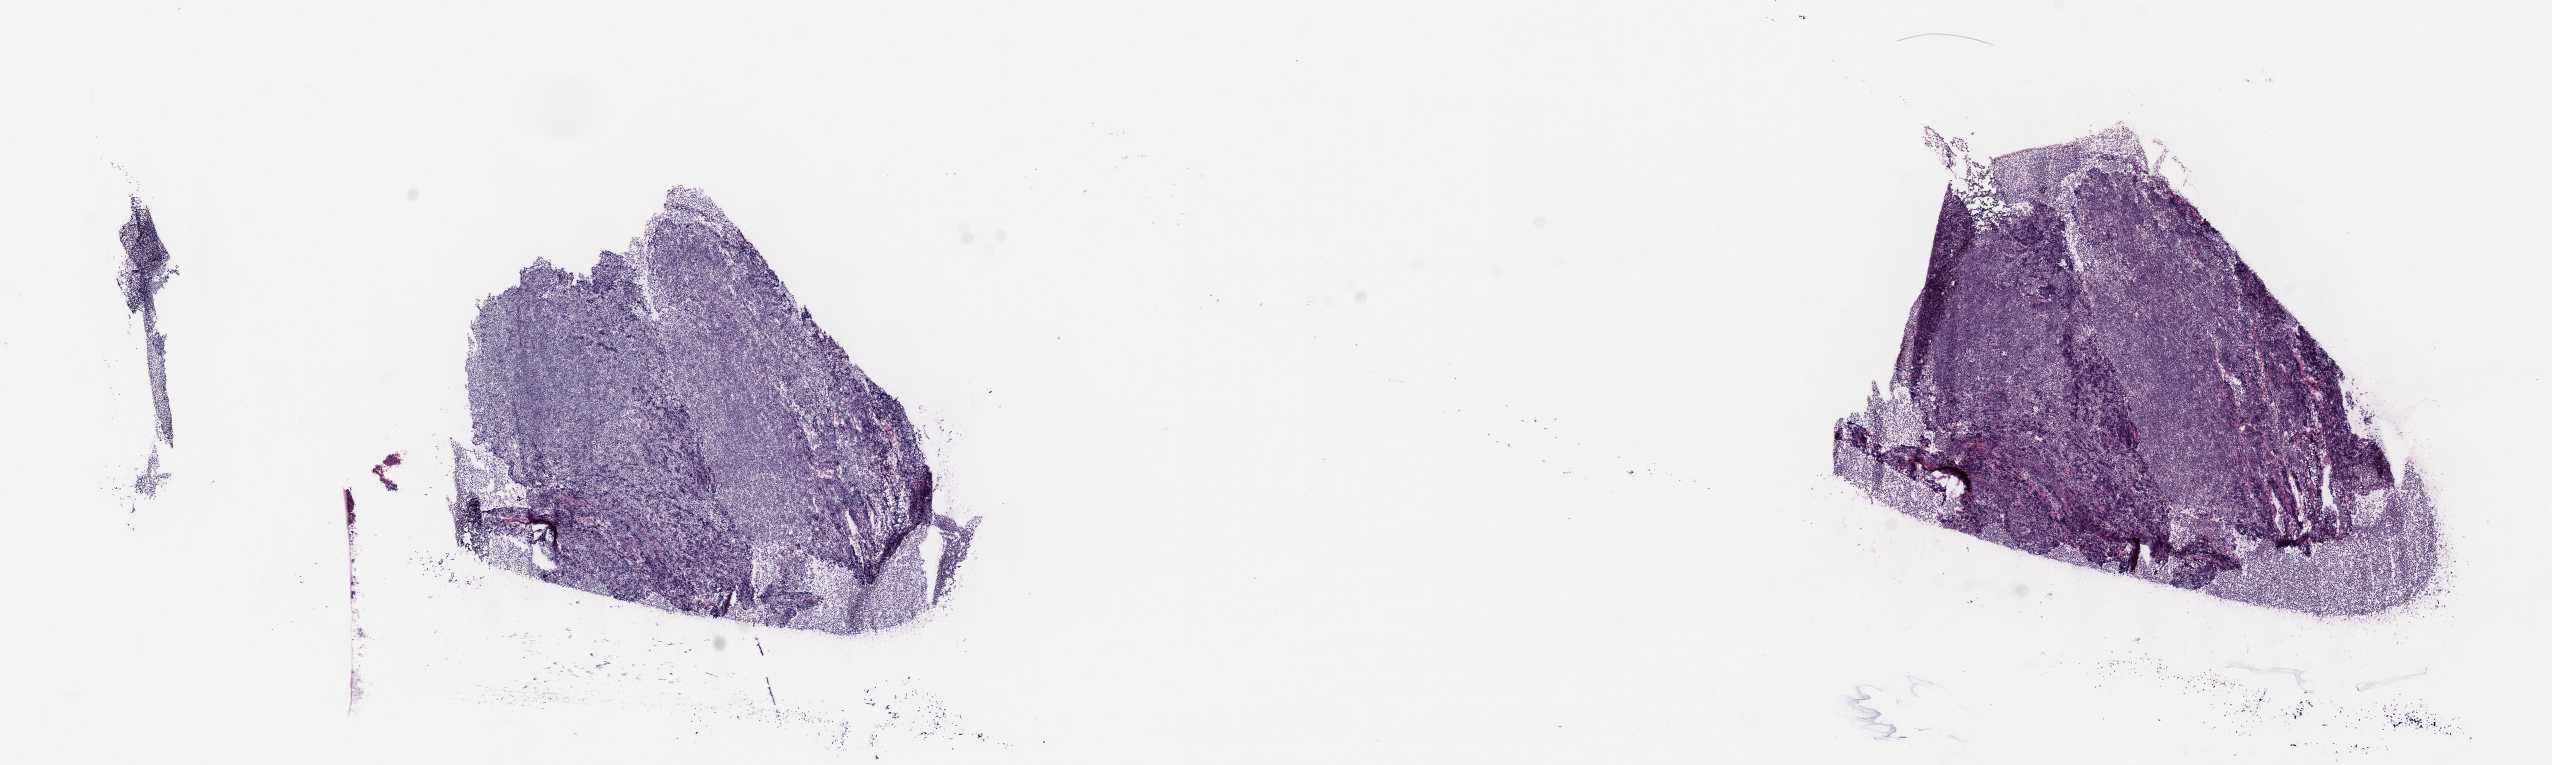
Digitized hematoxylin and eosin (H&E)-stained section — shown as a low-resolution overview of the whole scanned area (about 20.6 x 6.2 mm). Frozen section. Specimen: primary tumor. Anatomic site: cranium. Patient: female, age at initial diagnosis 8 years. Composition of this section per pathologist review: tumor cells 90%, tumor nuclei 90%, stromal cells 5%, necrosis 5%, normal cells 0%. Inflammatory infiltration, as recorded: lymphocyte infiltration 10%, monocyte infiltration 15%, neutrophil infiltration 5%.
Histologic diagnosis: Burkitt lymphoma, NOS. Ann Arbor stage (patient): Stage IV.